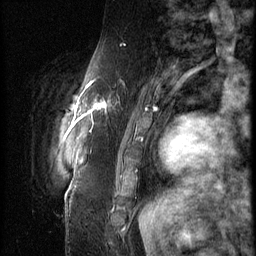
Breast MRI (dynamic contrast-enhanced), one sagittal slice. 3 images stored at this slice position (order not interpretable as contrast timing). 1.5 T. TE 4.2 ms, TR 9 ms. 256 × 256 image matrix, field of view 180 × 180 mm. Female patient, age 57 years. Case-level facts recorded for this patient, not image findings: setting: breast cancer imaged before/during neoadjuvant chemotherapy; receptor status: triple-negative.
Outlined on this slice (semi-automatically segmented with operator editing):
- analysis volume of interest (the breast-tissue region the enhancement analysis was run in; not a lesion): bounding box (x1, y1, x2, y2) in pixels: (86, 74, 138, 129)
- tumour enhancement mask (voxels above the 140 % enhancement threshold inside the analysis volume of interest): (86, 80, 107, 129)